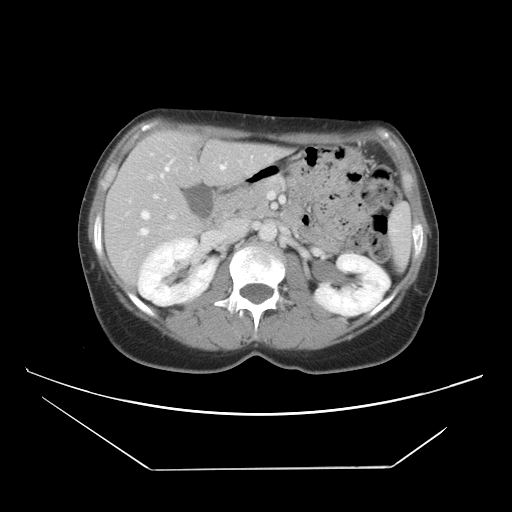
Contrast-enhanced abdominal CT, one axial slice. Slice 23 of 42 in the series (ordered by position). 120 kVp. Soft-tissue window (W 400 / L 40 HU). 5 mm slice thickness. 512 × 512 image matrix, field of view 399 × 399 mm. Female patient, age 52 years. From the clinical record (not read from this slice): diagnosis: colorectal cancer liver metastases, imaged before liver resection; multiple liver metastases: yes; largest metastasis: 5.5 cm.
Structures marked on this image (manually delineated by an expert):
- hepatic veins: box from (x=129, y=152) to (x=227, y=236) px
- liver: (x=106, y=131)–(x=285, y=281)
- planned liver remnant (the part of the liver to remain after resection): (x=114, y=131)–(x=218, y=210)
- portal vein (with intrahepatic branches): (x=153, y=159)–(x=270, y=219)